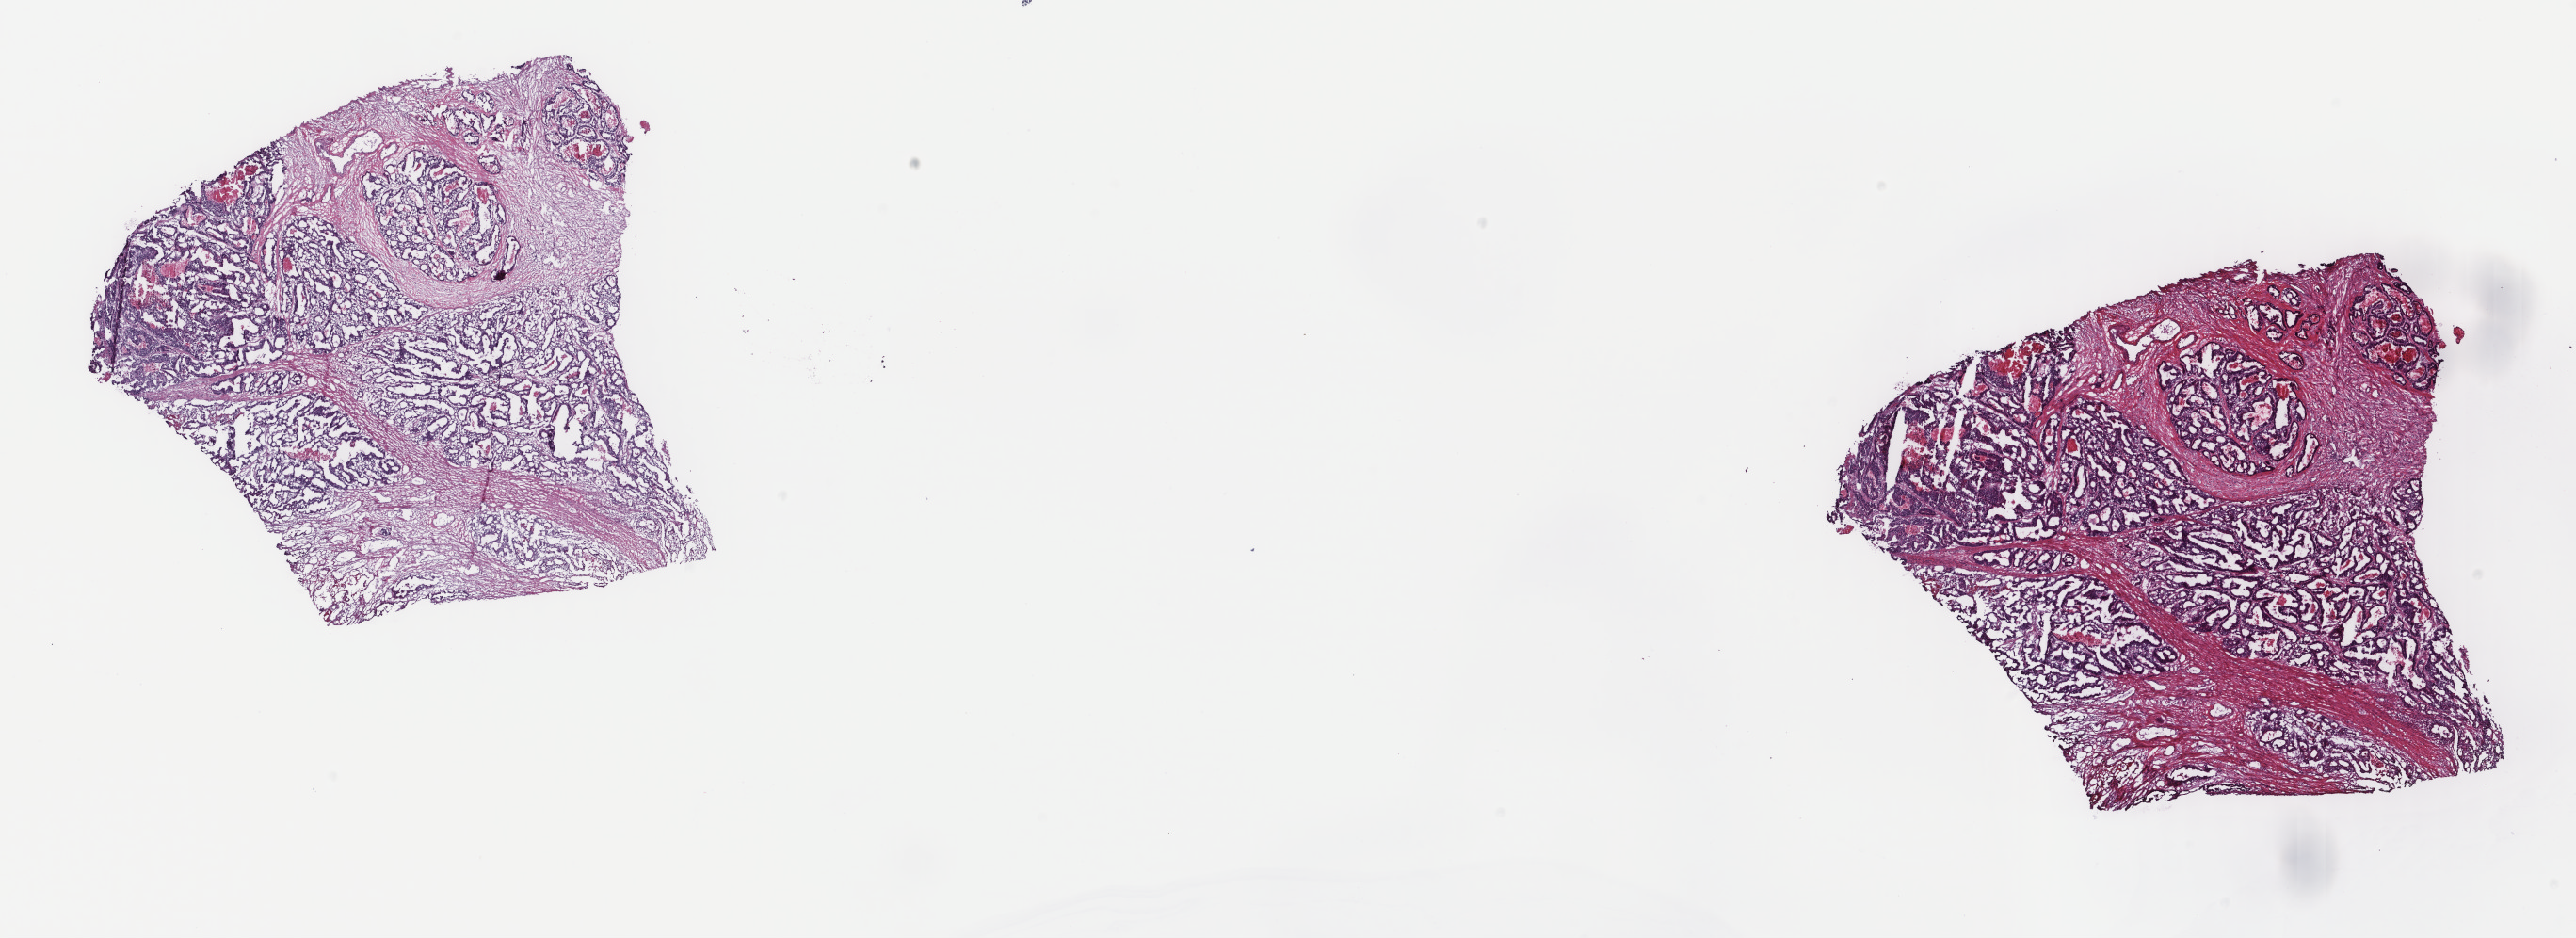
Hematoxylin and eosin (H&E) stained whole-slide image — low-resolution overview of the scanned area, about 21.7 x 7.9 mm. Frozen section from the top of the tissue portion. Rectum, primary tumour sample. Female, age 73 years at initial diagnosis. Slide review estimates, as recorded: tumour cells 90%, tumour nuclei 80%, normal cells 0%, stromal cells 0%, necrosis 10%. Inflammatory infiltration, as recorded: lymphocyte infiltration 0%, monocyte infiltration 0%, neutrophil infiltration 0%.
• AJCC pathologic stage: IIIC
• lymph nodes positive (case pathology): 5 of 15 examined
• histologic diagnosis: Adenocarcinoma, NOS (rectosigmoid junction)